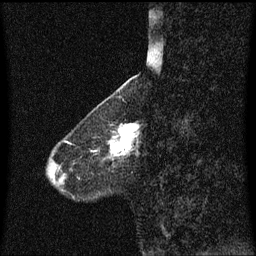
Breast MRI (dynamic contrast-enhanced), one sagittal slice. Dynamic contrast-enhanced series, image 2 of 3 at this slice position (ordered by acquisition). 1.5 T. TE 4.2 ms, TR 8.4 ms. 256 × 256 image matrix, field of view 200 × 200 mm. Patient: female, 58 years.
Annotated regions visible in this slice (semi-automatically segmented with operator editing):
- analysis volume of interest (the breast-tissue region the enhancement analysis was run in; not a lesion): bounding box [x1, y1, x2, y2] px = [108, 123, 139, 160]
- tumour enhancement mask (voxels above the 70 % enhancement threshold inside the analysis volume of interest): [110, 124, 139, 156]